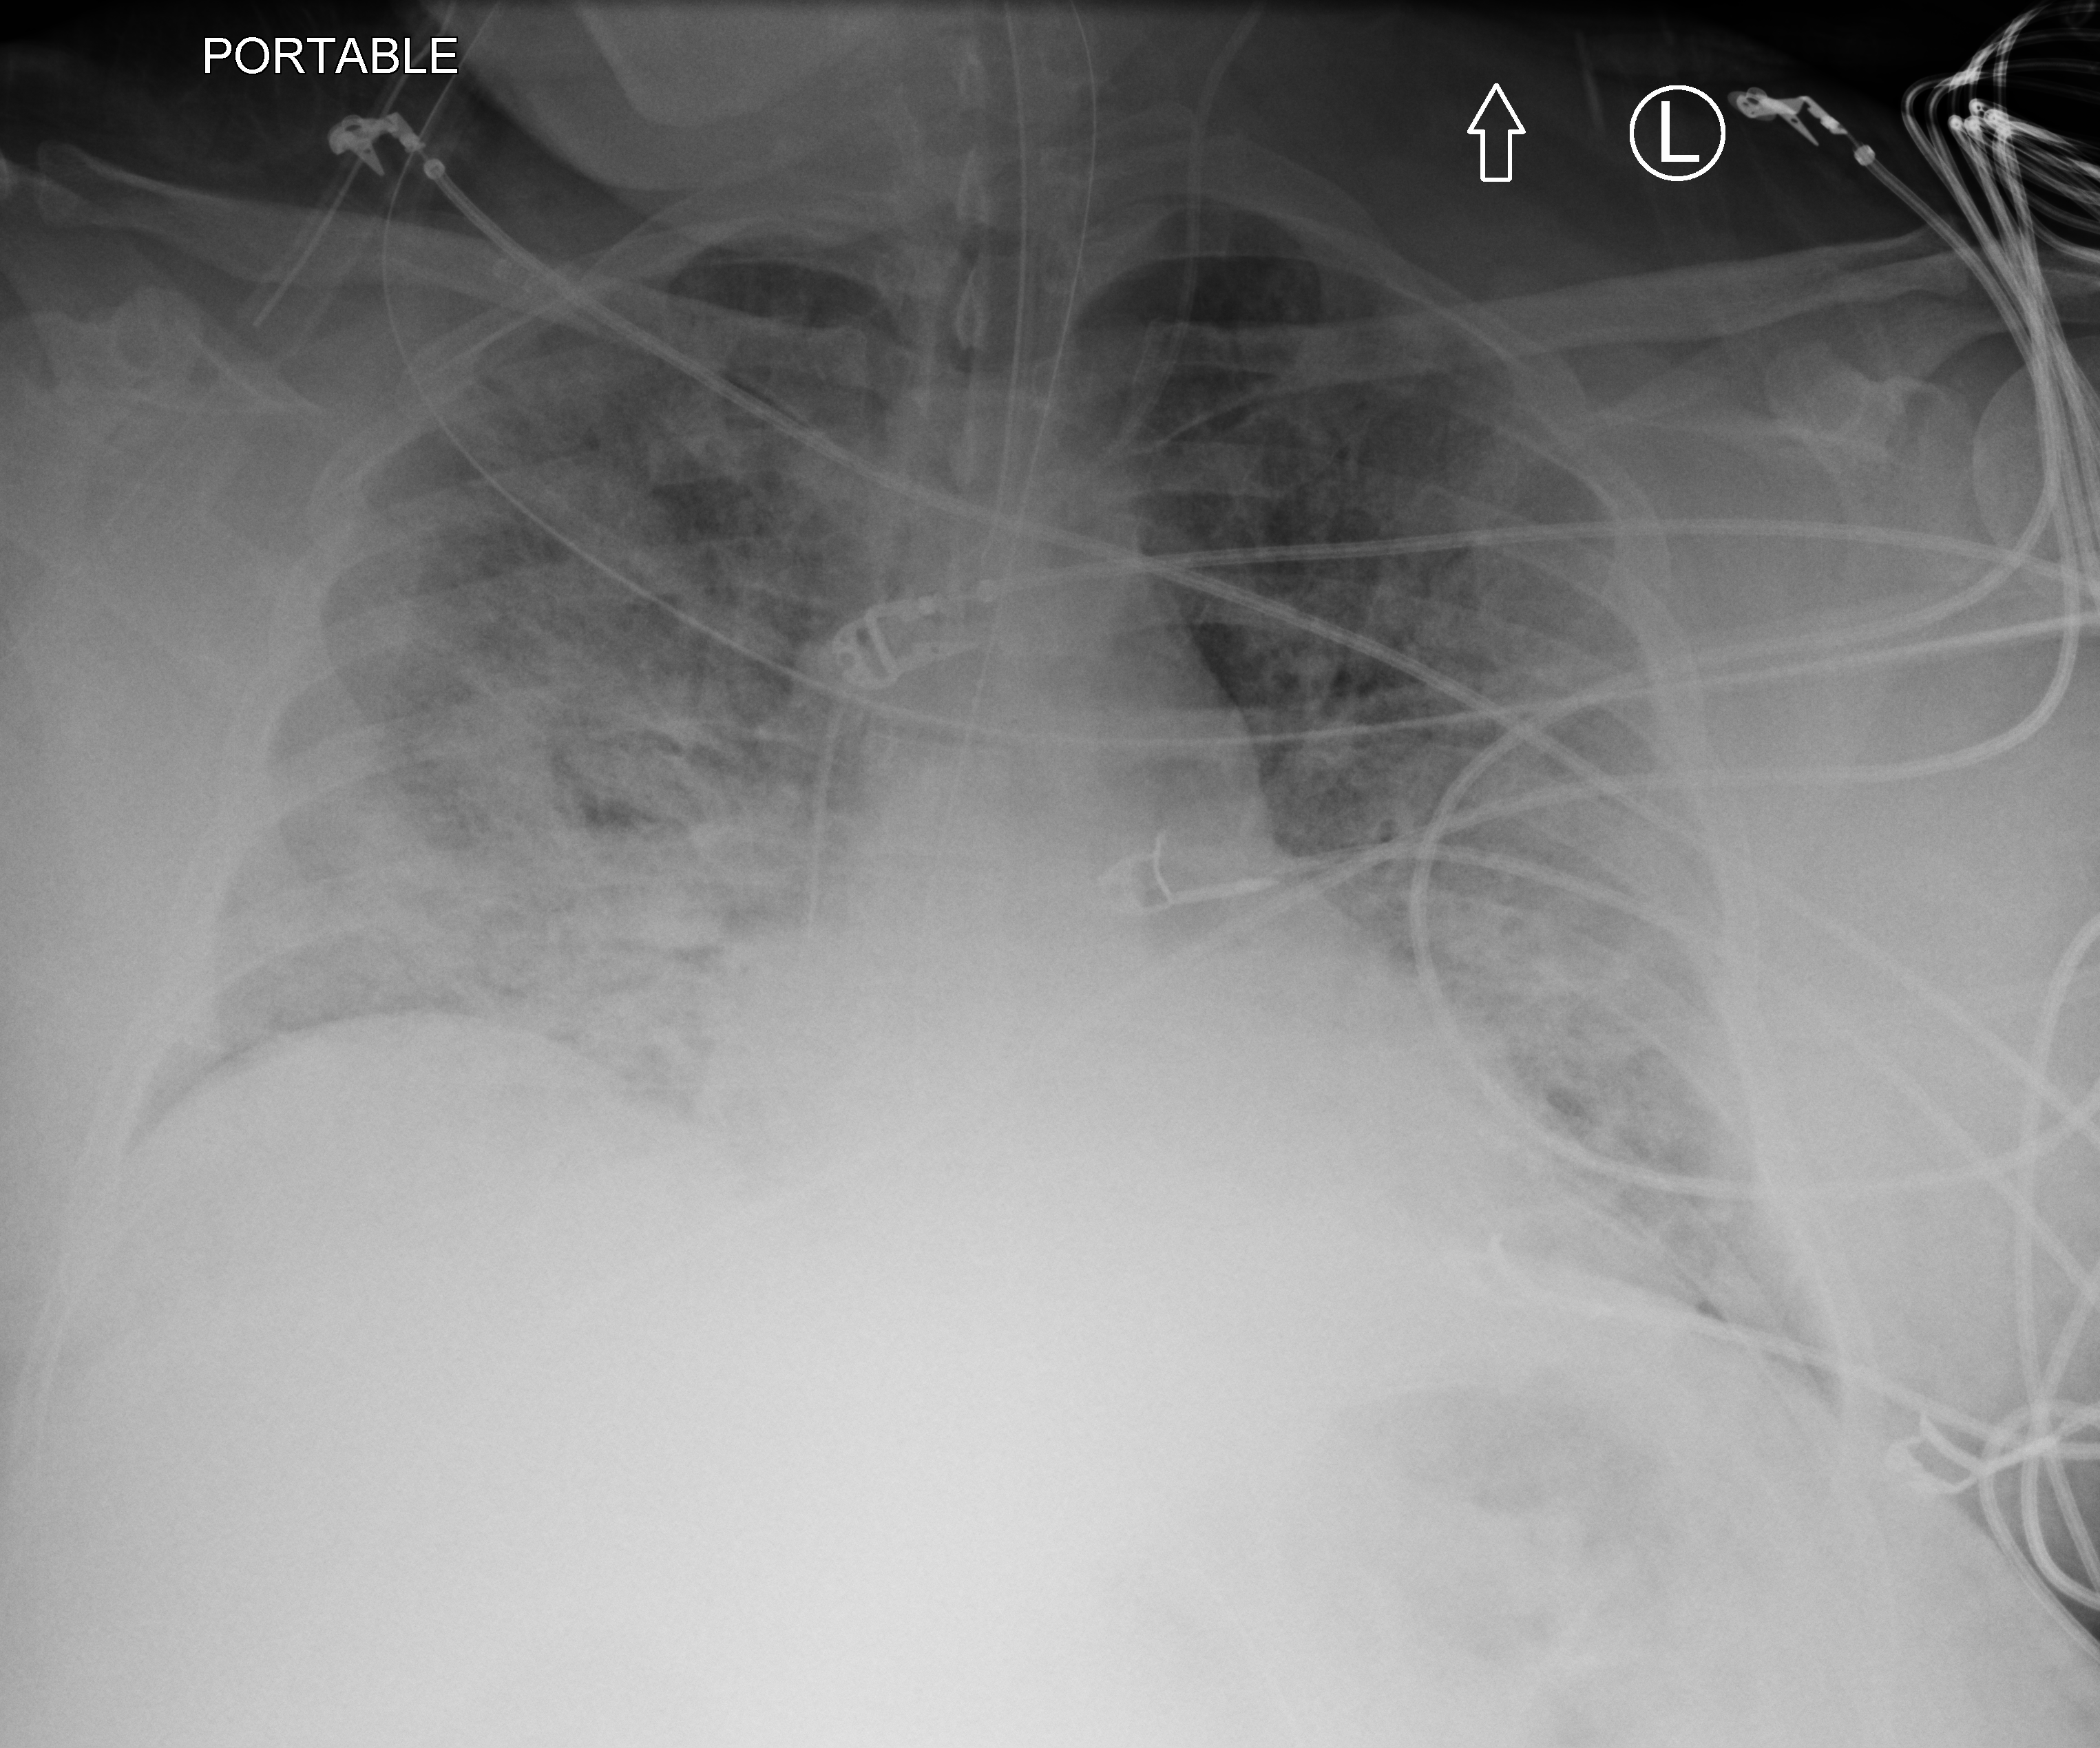
Portable chest radiograph, anteroposterior (AP) projection. Adult patient hospitalised with COVID-19, age 18–59 years.
Admission-level facts for this patient (not findings on this image; timing relative to this image not recorded): other chronic lung disease (admission record): yes.